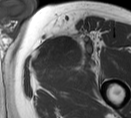
MRI of an extremity soft-tissue mass, one axial slice. Slice 54 of 55 in the series (ordered by position). MR volume resampled by the dataset authors to the PET/CT grid (not the native acquisition matrix). 3.27 mm slice thickness. 131 × 118 image matrix. Male patient. Case-level facts recorded for this patient, not image findings: histological type: pleiomorphic liposarcoma; grade: high; site of the primary tumour: left thigh.
Structures marked on this image (expert contour drawn on MRI and transferred to this co-registered scan by the dataset authors):
- gross tumour volume including surrounding oedema: box from (x=34, y=29) to (x=97, y=67) px
- gross tumour volume (mass): (x=34, y=36)–(x=72, y=65)